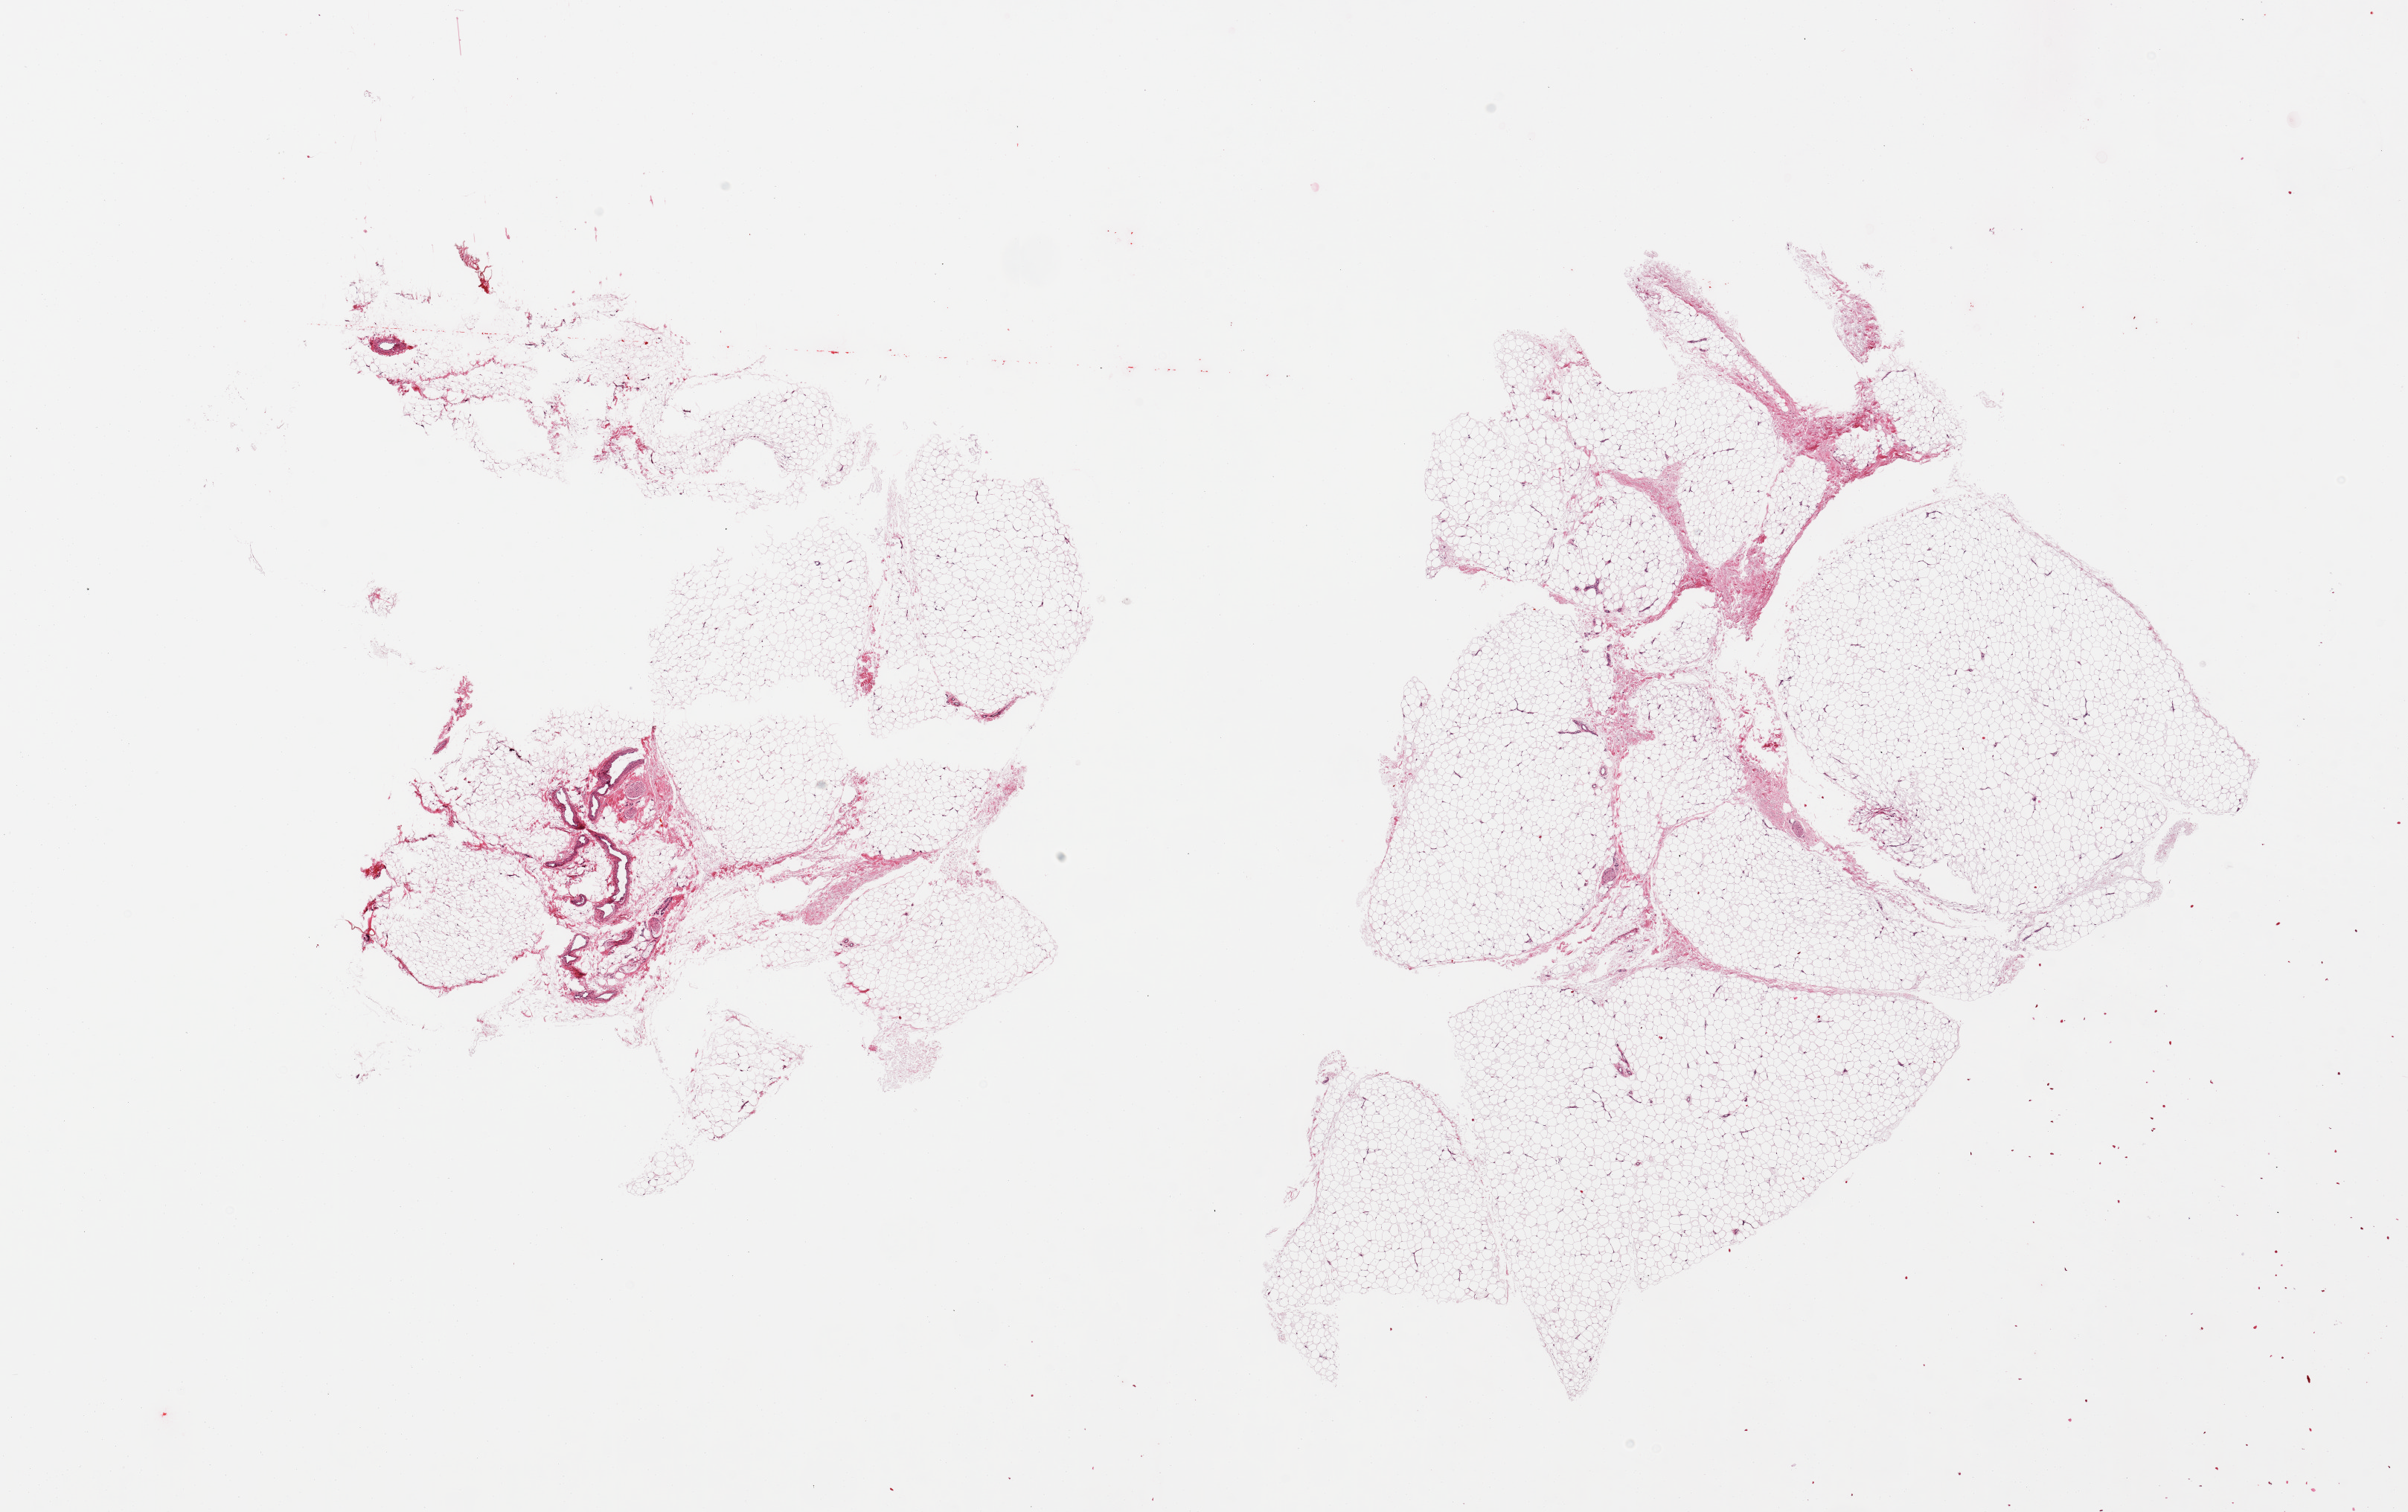
Whole-slide image, hematoxylin and eosin (H&E) stain — a low-resolution overview of the entire scanned area, about 25.6 x 16.1 mm. PAXgene-fixed paraffin-embedded (PFPE) section. Sampled site (target tissue): adipose tissue. Donor tissue sample.
Review note (as recorded): 2 pieces; includes some vessels and nerves centrally.